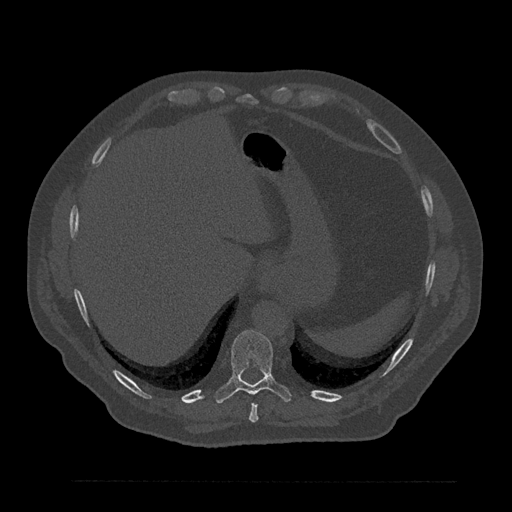
CT including the spine, one axial slice. Slice 357 of 797 in the series (ordered by position). Reconstruction kernel Br40s/3. 120 kVp. Bone window (W 1800 / L 400 HU). 512 × 512 image matrix. Patient: male, 61 years. From the clinical record (not read from this slice): primary cancer: prostate.
Annotated regions visible in this slice (semi-automatic segmentation, software-assisted and operator-edited):
- T10 vertebra: bounding box <215,330,291,403> (left, top, right, bottom; pixels)
- T9 vertebra: <249,403,259,423>